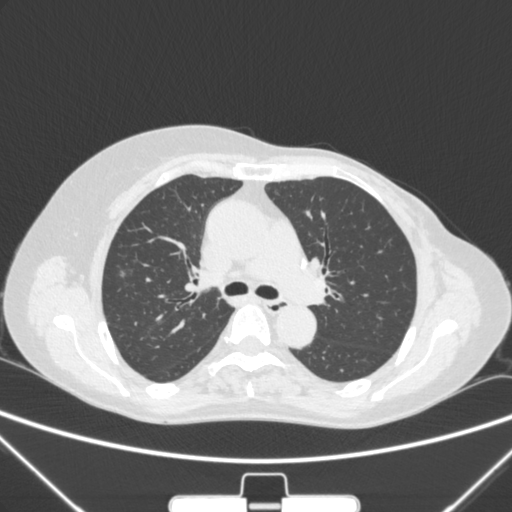
Chest CT, one axial slice. Position 164 of 265 along the scan axis. 120 kVp. Lung window (W 1500 / L -600 HU). 1 mm slice thickness. 512 × 512 image matrix. Patient: female, 64 years. From the clinical record (not read from this slice): clinical TNM (as recorded): T1c N0 M0.
Structures marked on this image (rectangle marked by the reading radiologist):
- lung tumour (recorded histology: adenocarcinoma): bounding box (x1, y1, x2, y2) in pixels: (109, 260, 137, 290)